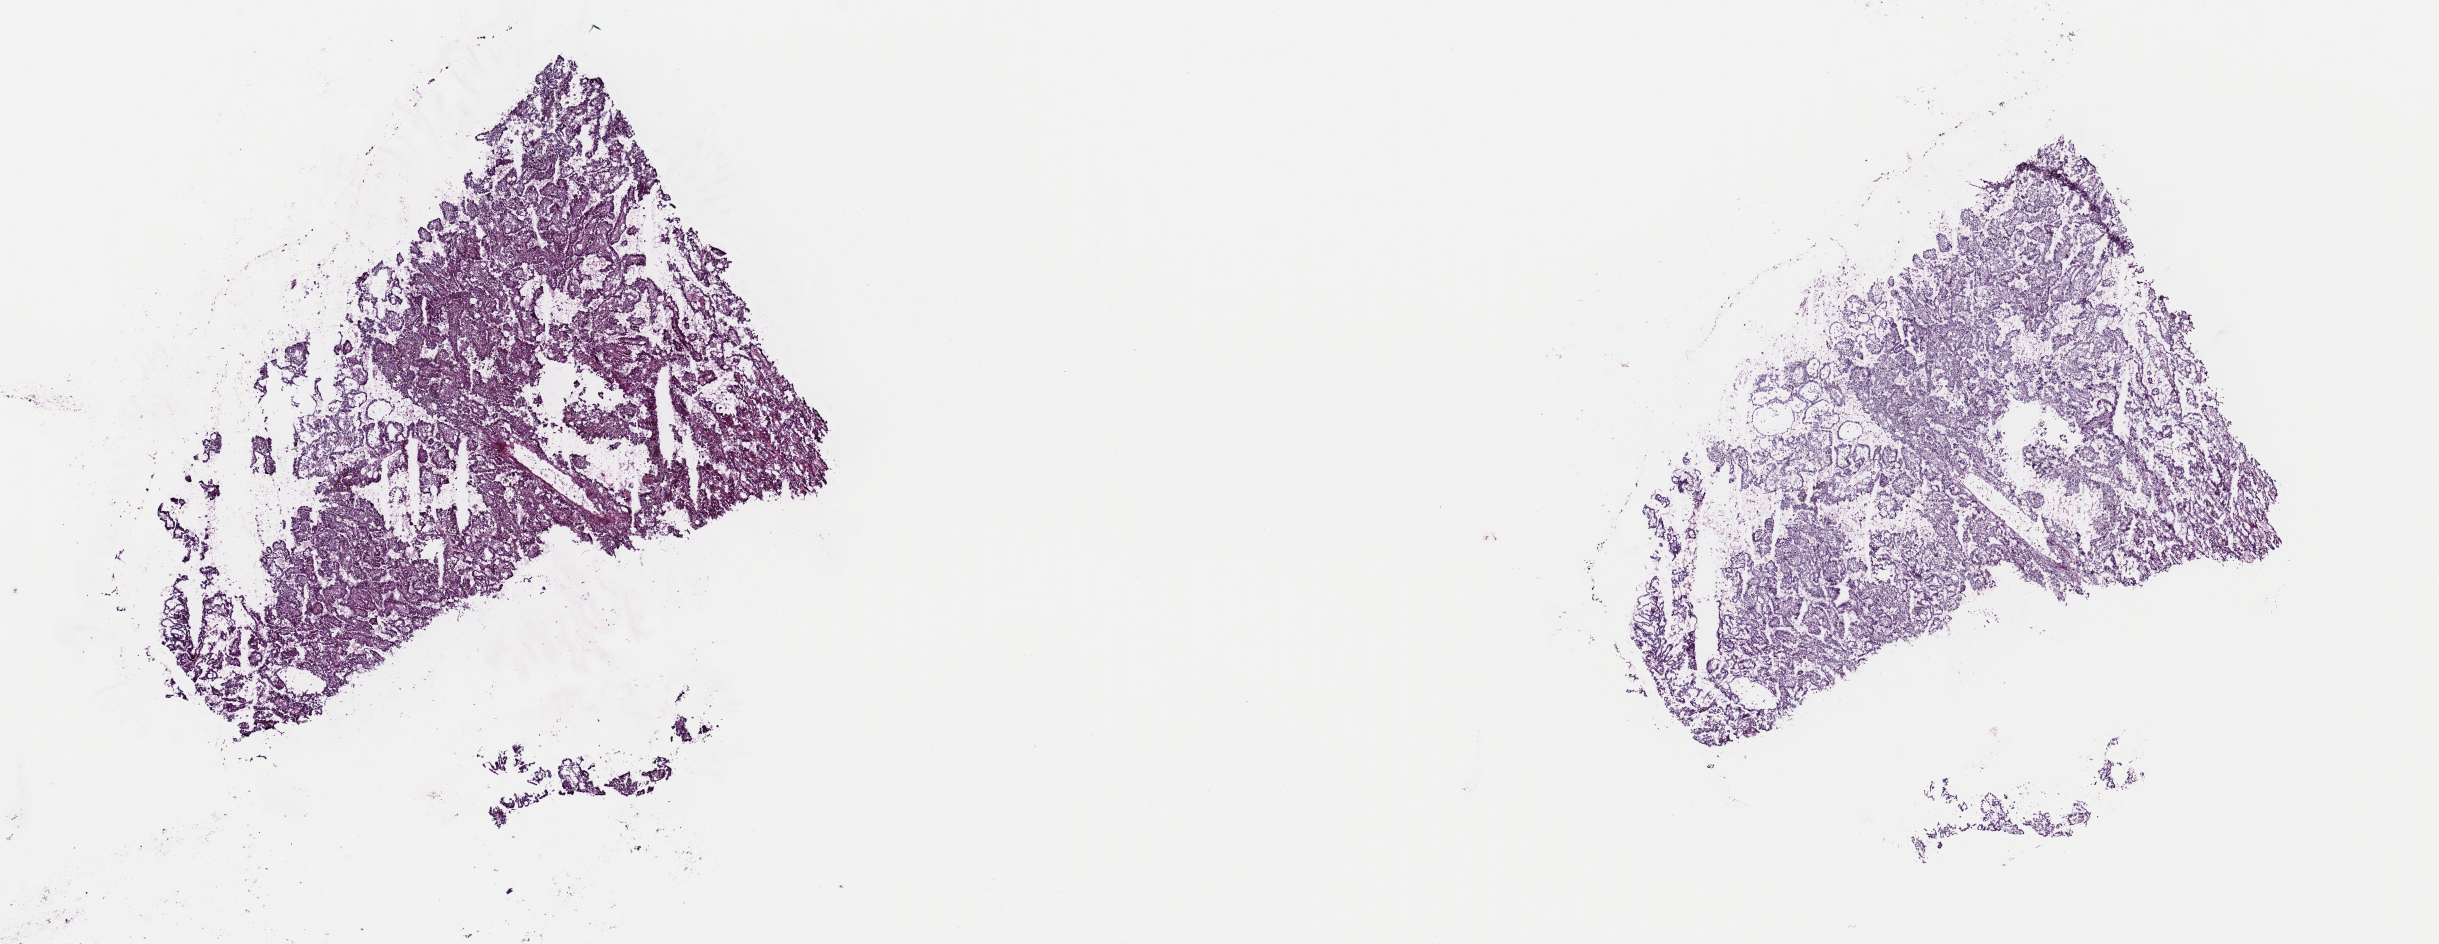
Digitized H&E-stained tissue section (whole slide) — shown as a low-resolution overview of the whole scanned area (about 19.3 x 7.5 mm, acquisition: 40x scan), frozen section, primary tumour sample from the kidney. Male patient; age at initial diagnosis 69 years. Composition of this section per pathologist review: tumour cells 90%, tumour nuclei 85%, normal cells 0%, stromal cells 10%, necrosis 0%. Infiltration values recorded for this section: lymphocyte infiltration 10%, monocyte infiltration 90%, neutrophil infiltration 0%.
* laterality: right
* histologic diagnosis: Papillary adenocarcinoma, NOS
* AJCC pathologic stage: I